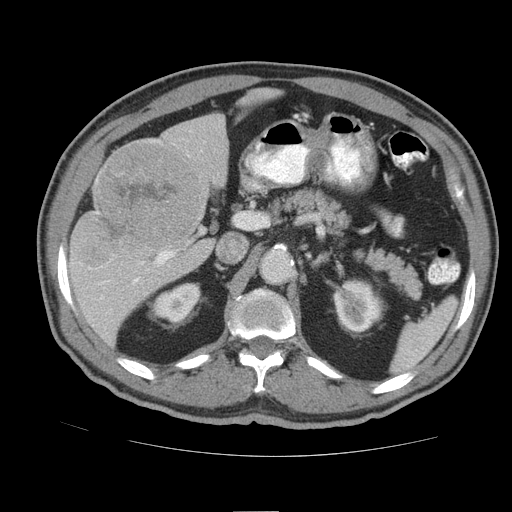
Contrast-enhanced abdominal CT (liver protocol), one axial slice. Position 49 of 105 along the scan axis. Soft-tissue window (W 400 / L 40 HU). 2.5 mm slice thickness. 512 × 512 image matrix, field of view 380 × 380 mm. Case-level facts recorded for this patient, not image findings: diagnosis: hepatocellular carcinoma (patient treated with transarterial chemoembolisation; whether this scan precedes or follows treatment is not stated here); TNM stage (as recorded): Stage-IIIB; Child-Pugh class: A.
Structures marked on this image (semi-automatically segmented with operator editing):
- liver parenchyma outside the tumour (the mass and vessels are separate outlines, so this box may not span the whole liver): box from (x=68, y=114) to (x=228, y=346) px
- mass: (x=73, y=142)–(x=200, y=263)
- liver vessels: (x=88, y=251)–(x=175, y=298)